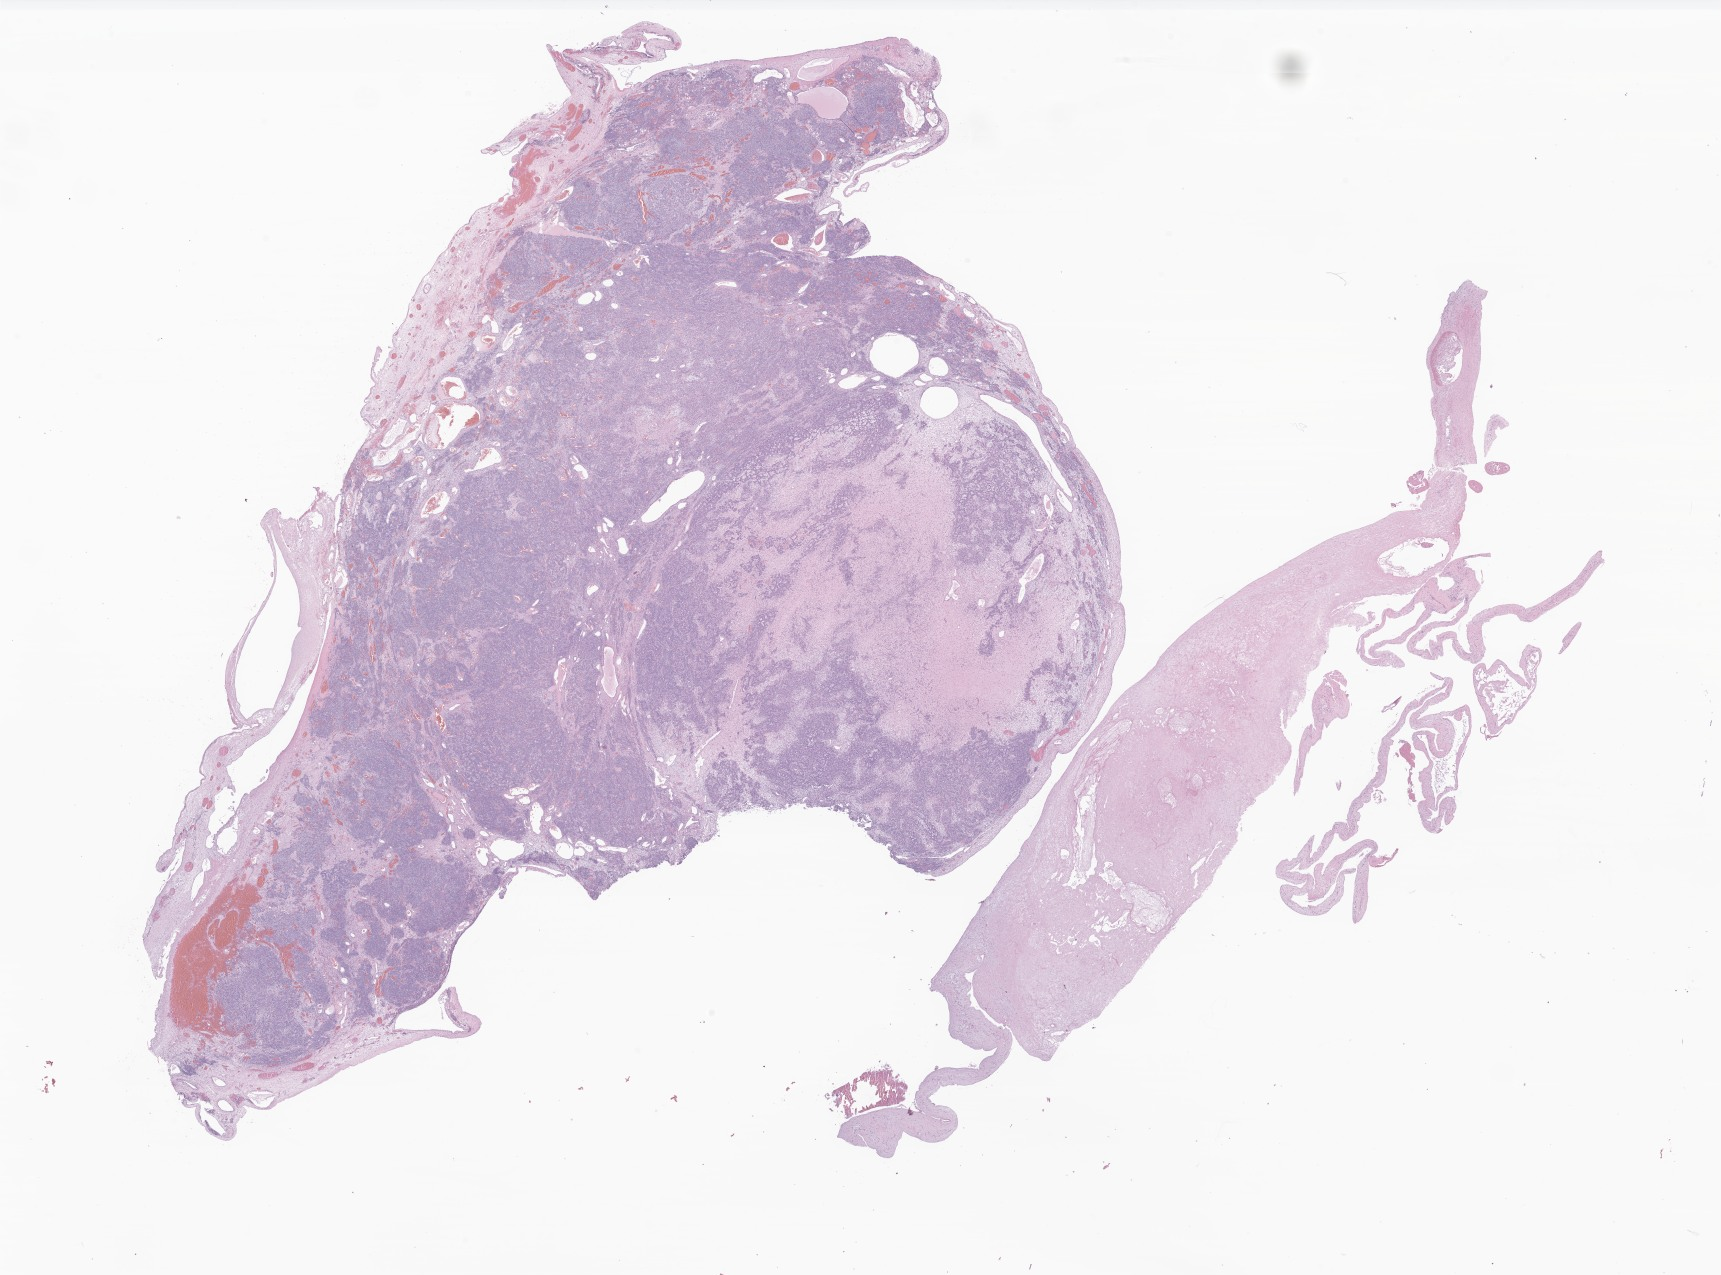
Digitized haematoxylin and eosin-stained section of tumor tissue from the ovary, whole scanned area (about 29.0 x 21.5 mm) shown as a low-resolution overview; formalin-fixed, paraffin-embedded (FFPE) tissue. Patient female; age 184 months (15 years 4 months).
Recorded diagnosis: Granulosa cell tumor, juvenile.